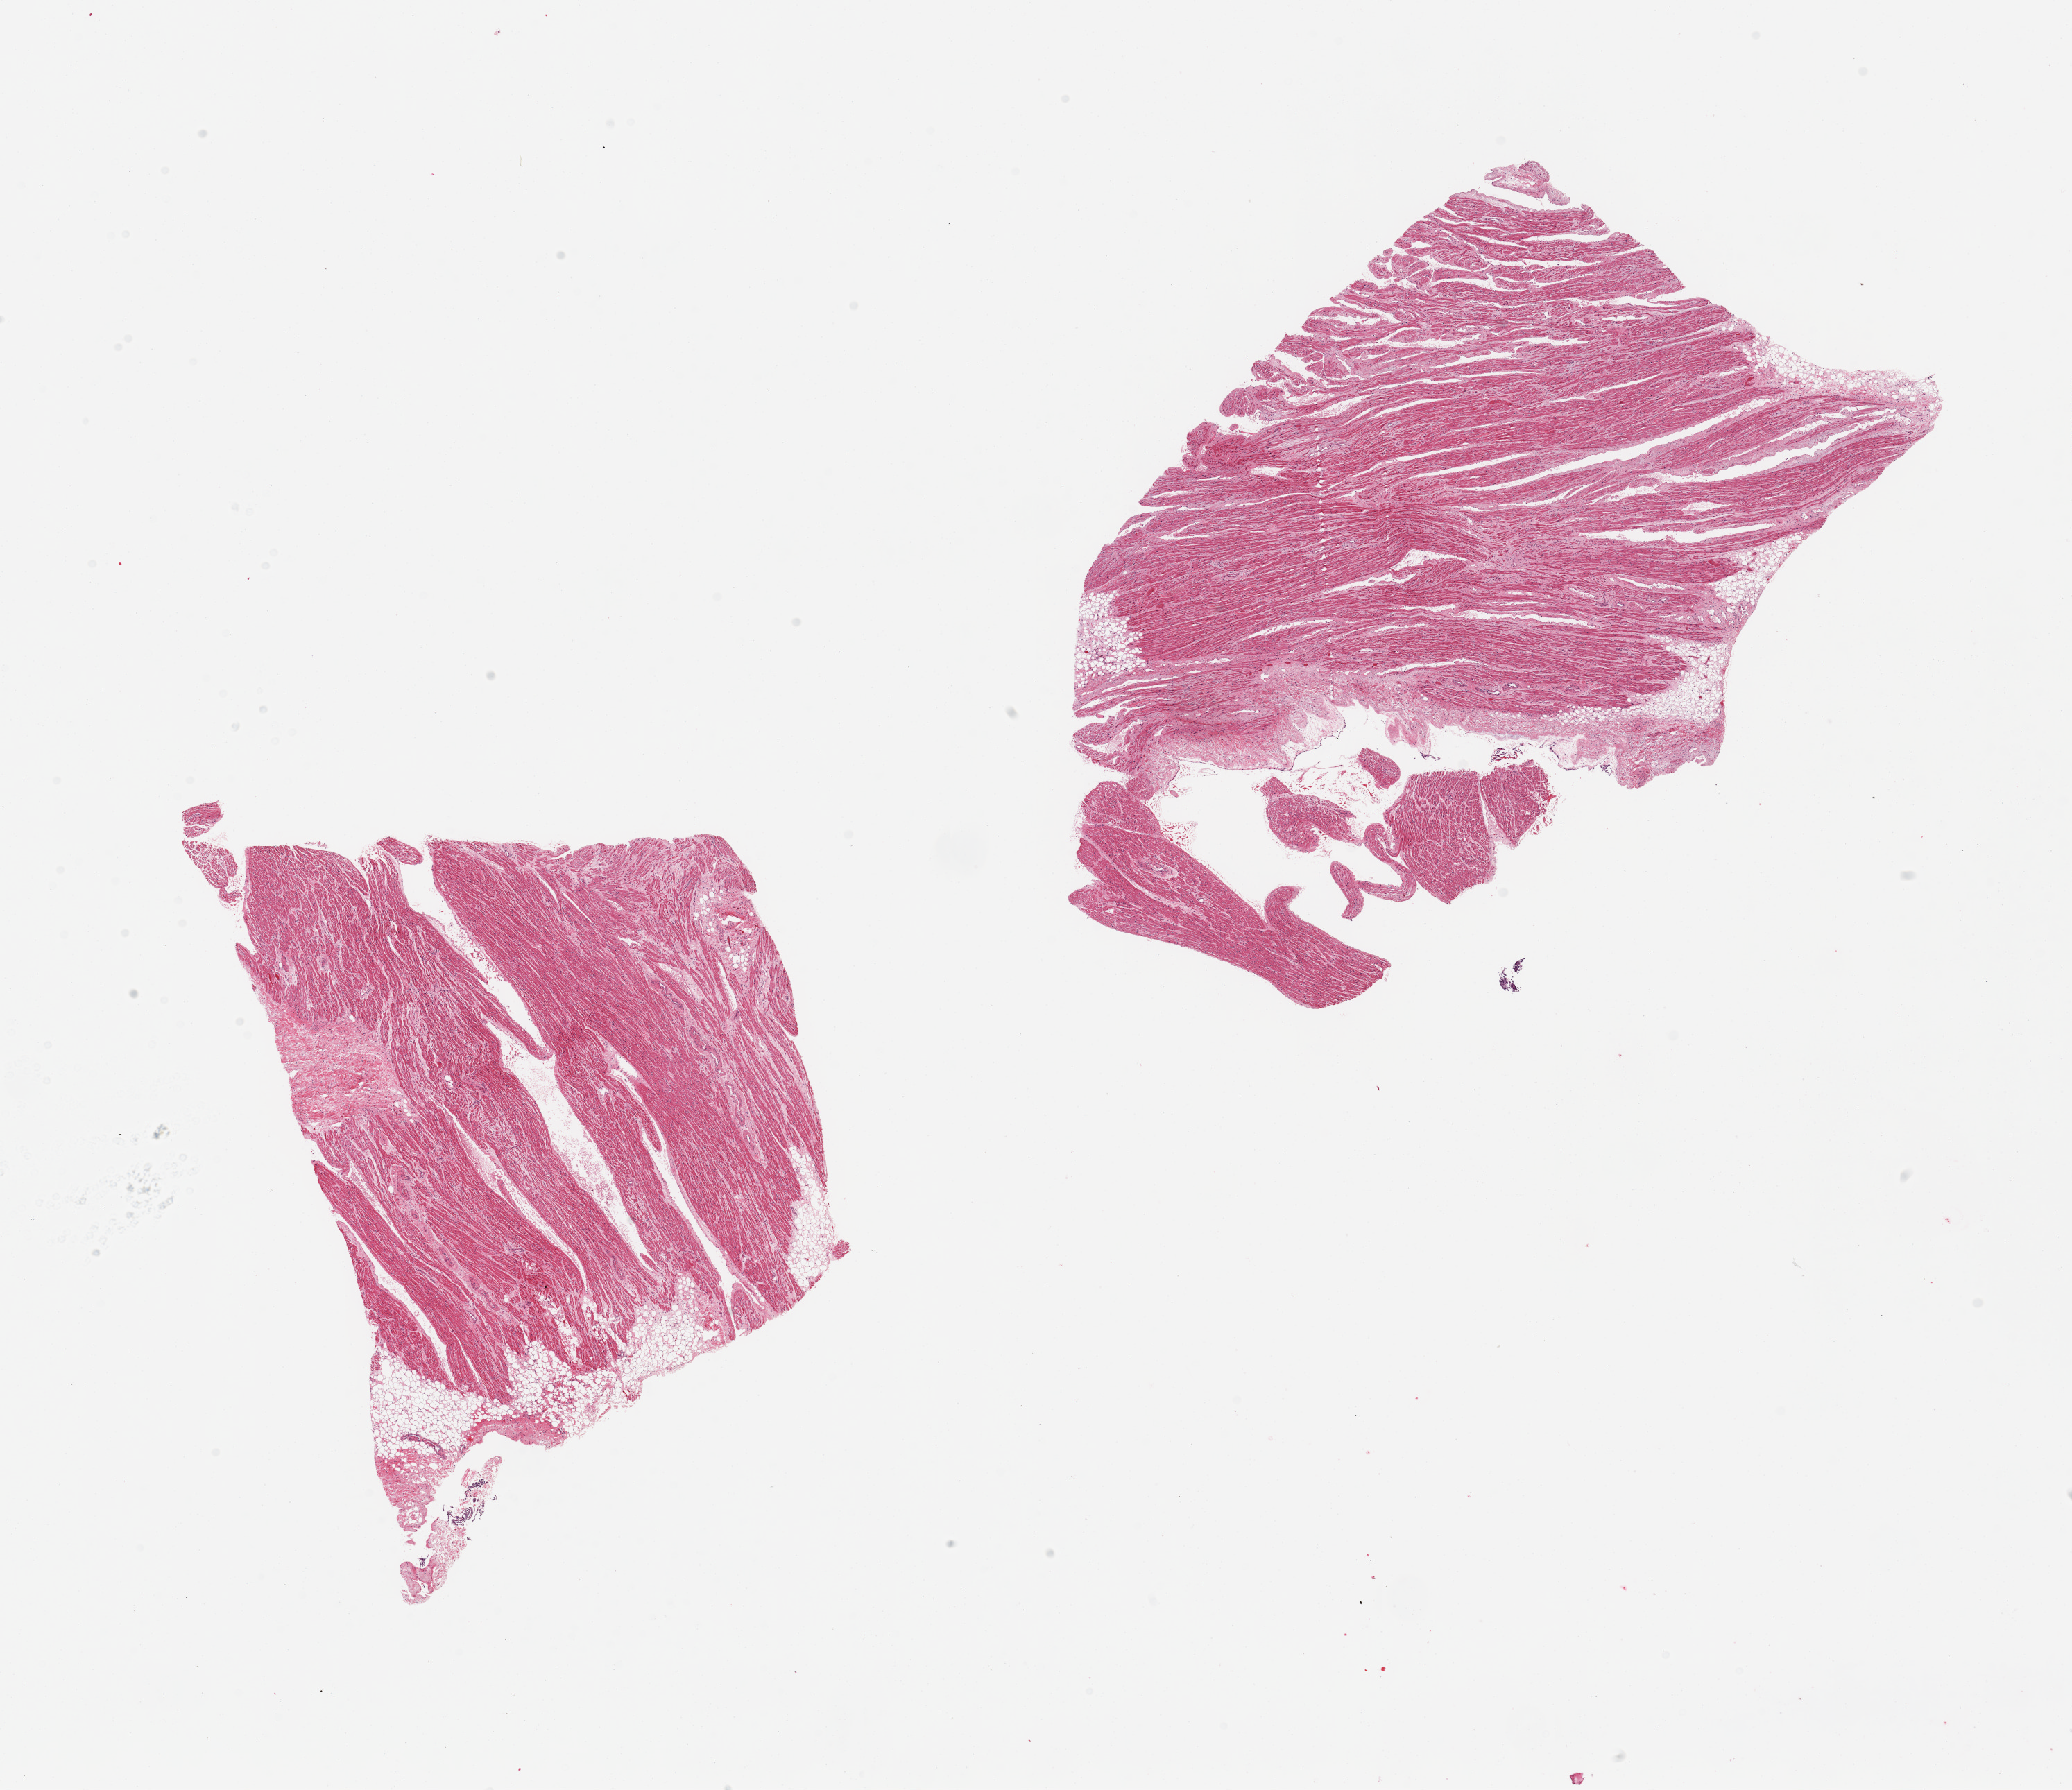
Haematoxylin and eosin whole-slide image, shown as a low-resolution overview of the whole scanned area (about 23.6 x 20.4 mm). PAXgene-fixed, paraffin-embedded tissue. Sampled site (target tissue): auricular appendage. Donor tissue sample.
Reviewer comment on this tissue sample: 2 pieces; small amount of internal and external fat.